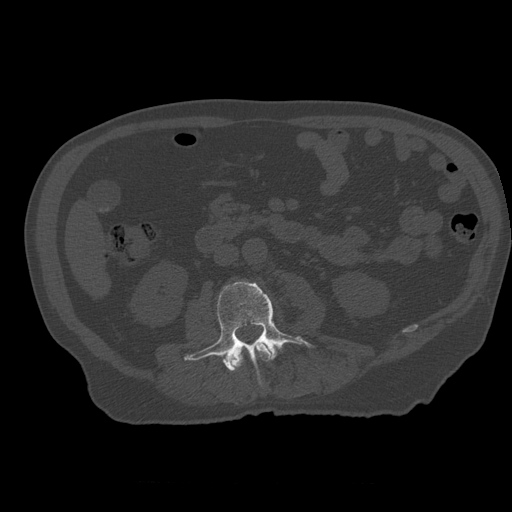
CT including the spine, one axial slice; slice 193 of 399 in the series (ordered by position); bone window (W 1800 / L 400 HU); 512 × 512 image matrix, field of view 407 × 407 mm. Patient age 73 years. From the clinical record (not read from this slice): primary cancer: prostate; vertebrae with lytic lesions (as recorded): L2.
Structures marked on this image (semi-automatically segmented with operator editing):
- L2 vertebra: bounding box <232,342,272,370> (left, top, right, bottom; pixels)
- L3 vertebra: <184,282,311,372>